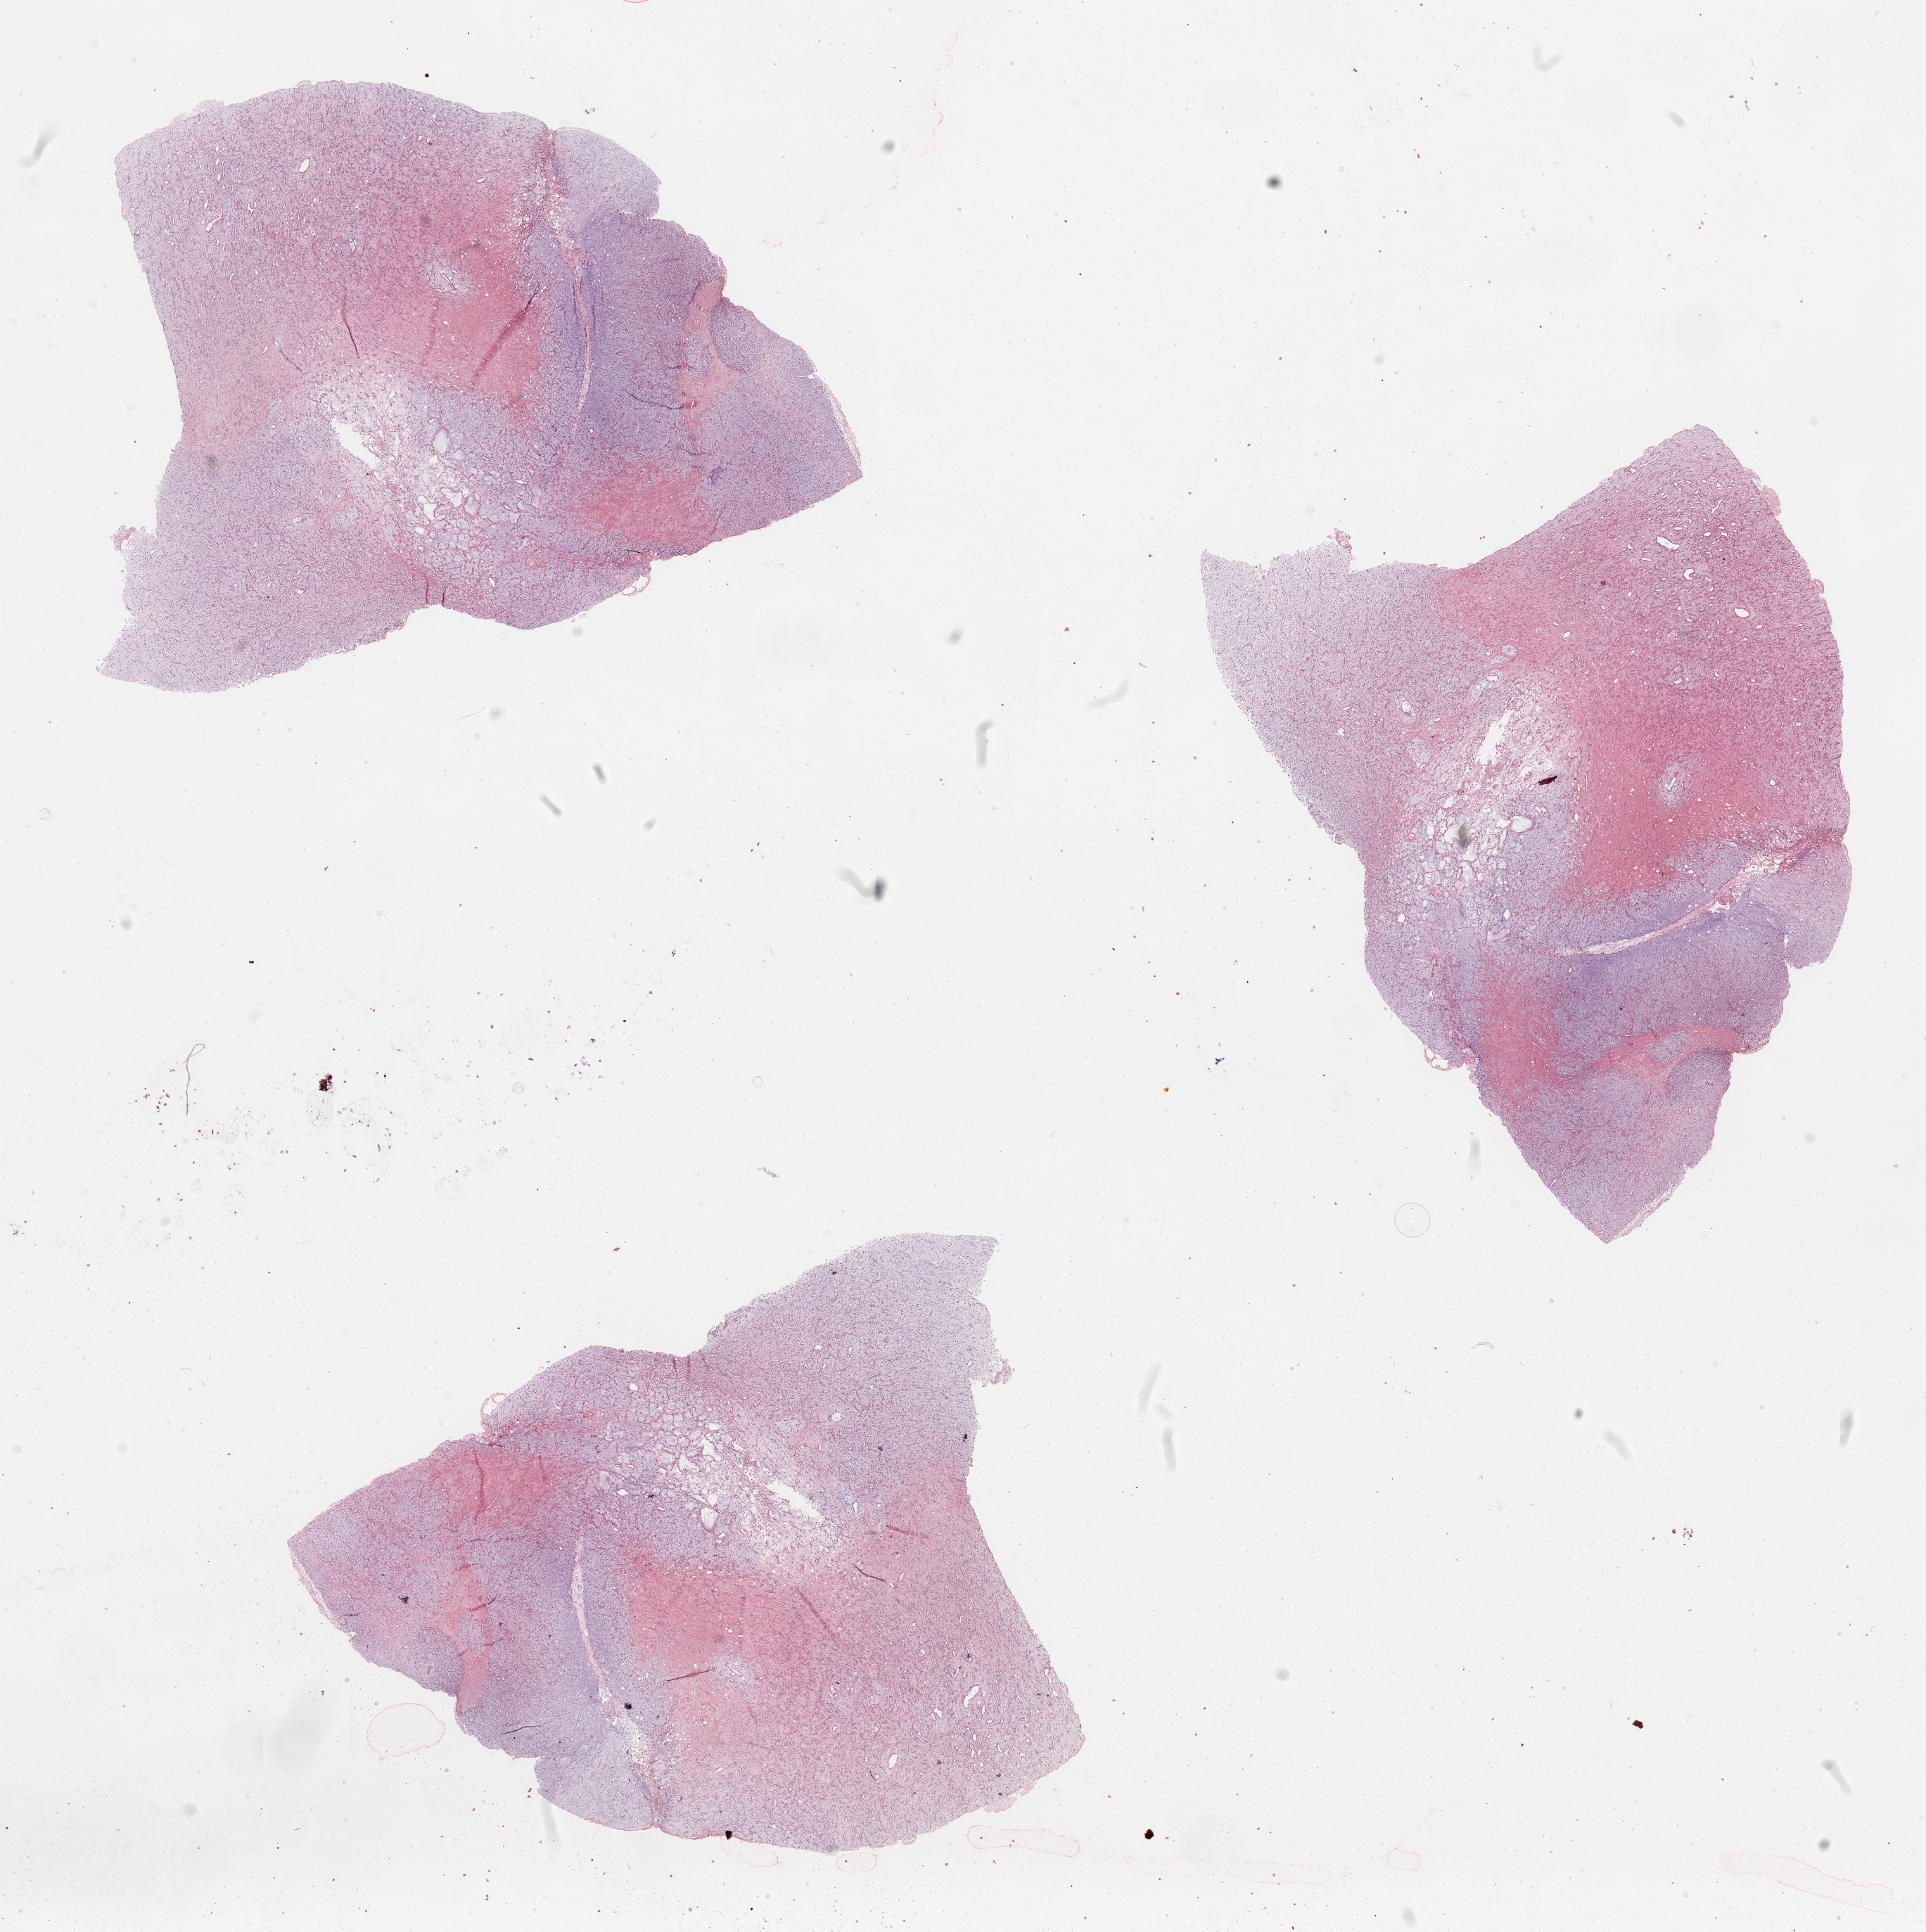
Digitized Hematoxylin and eosin (H&E) stained tissue section (whole slide) — shown as a low-resolution overview of the whole scanned area (about 21.7 x 21.7 mm, acquisition: 20x scan). Tumour tissue sample. Patient: male, age 42 years.
• primary tumour site (as recorded): lower extremity
• patient diagnosis (cohort enrolment): sarcoma (site not recorded at cohort level)